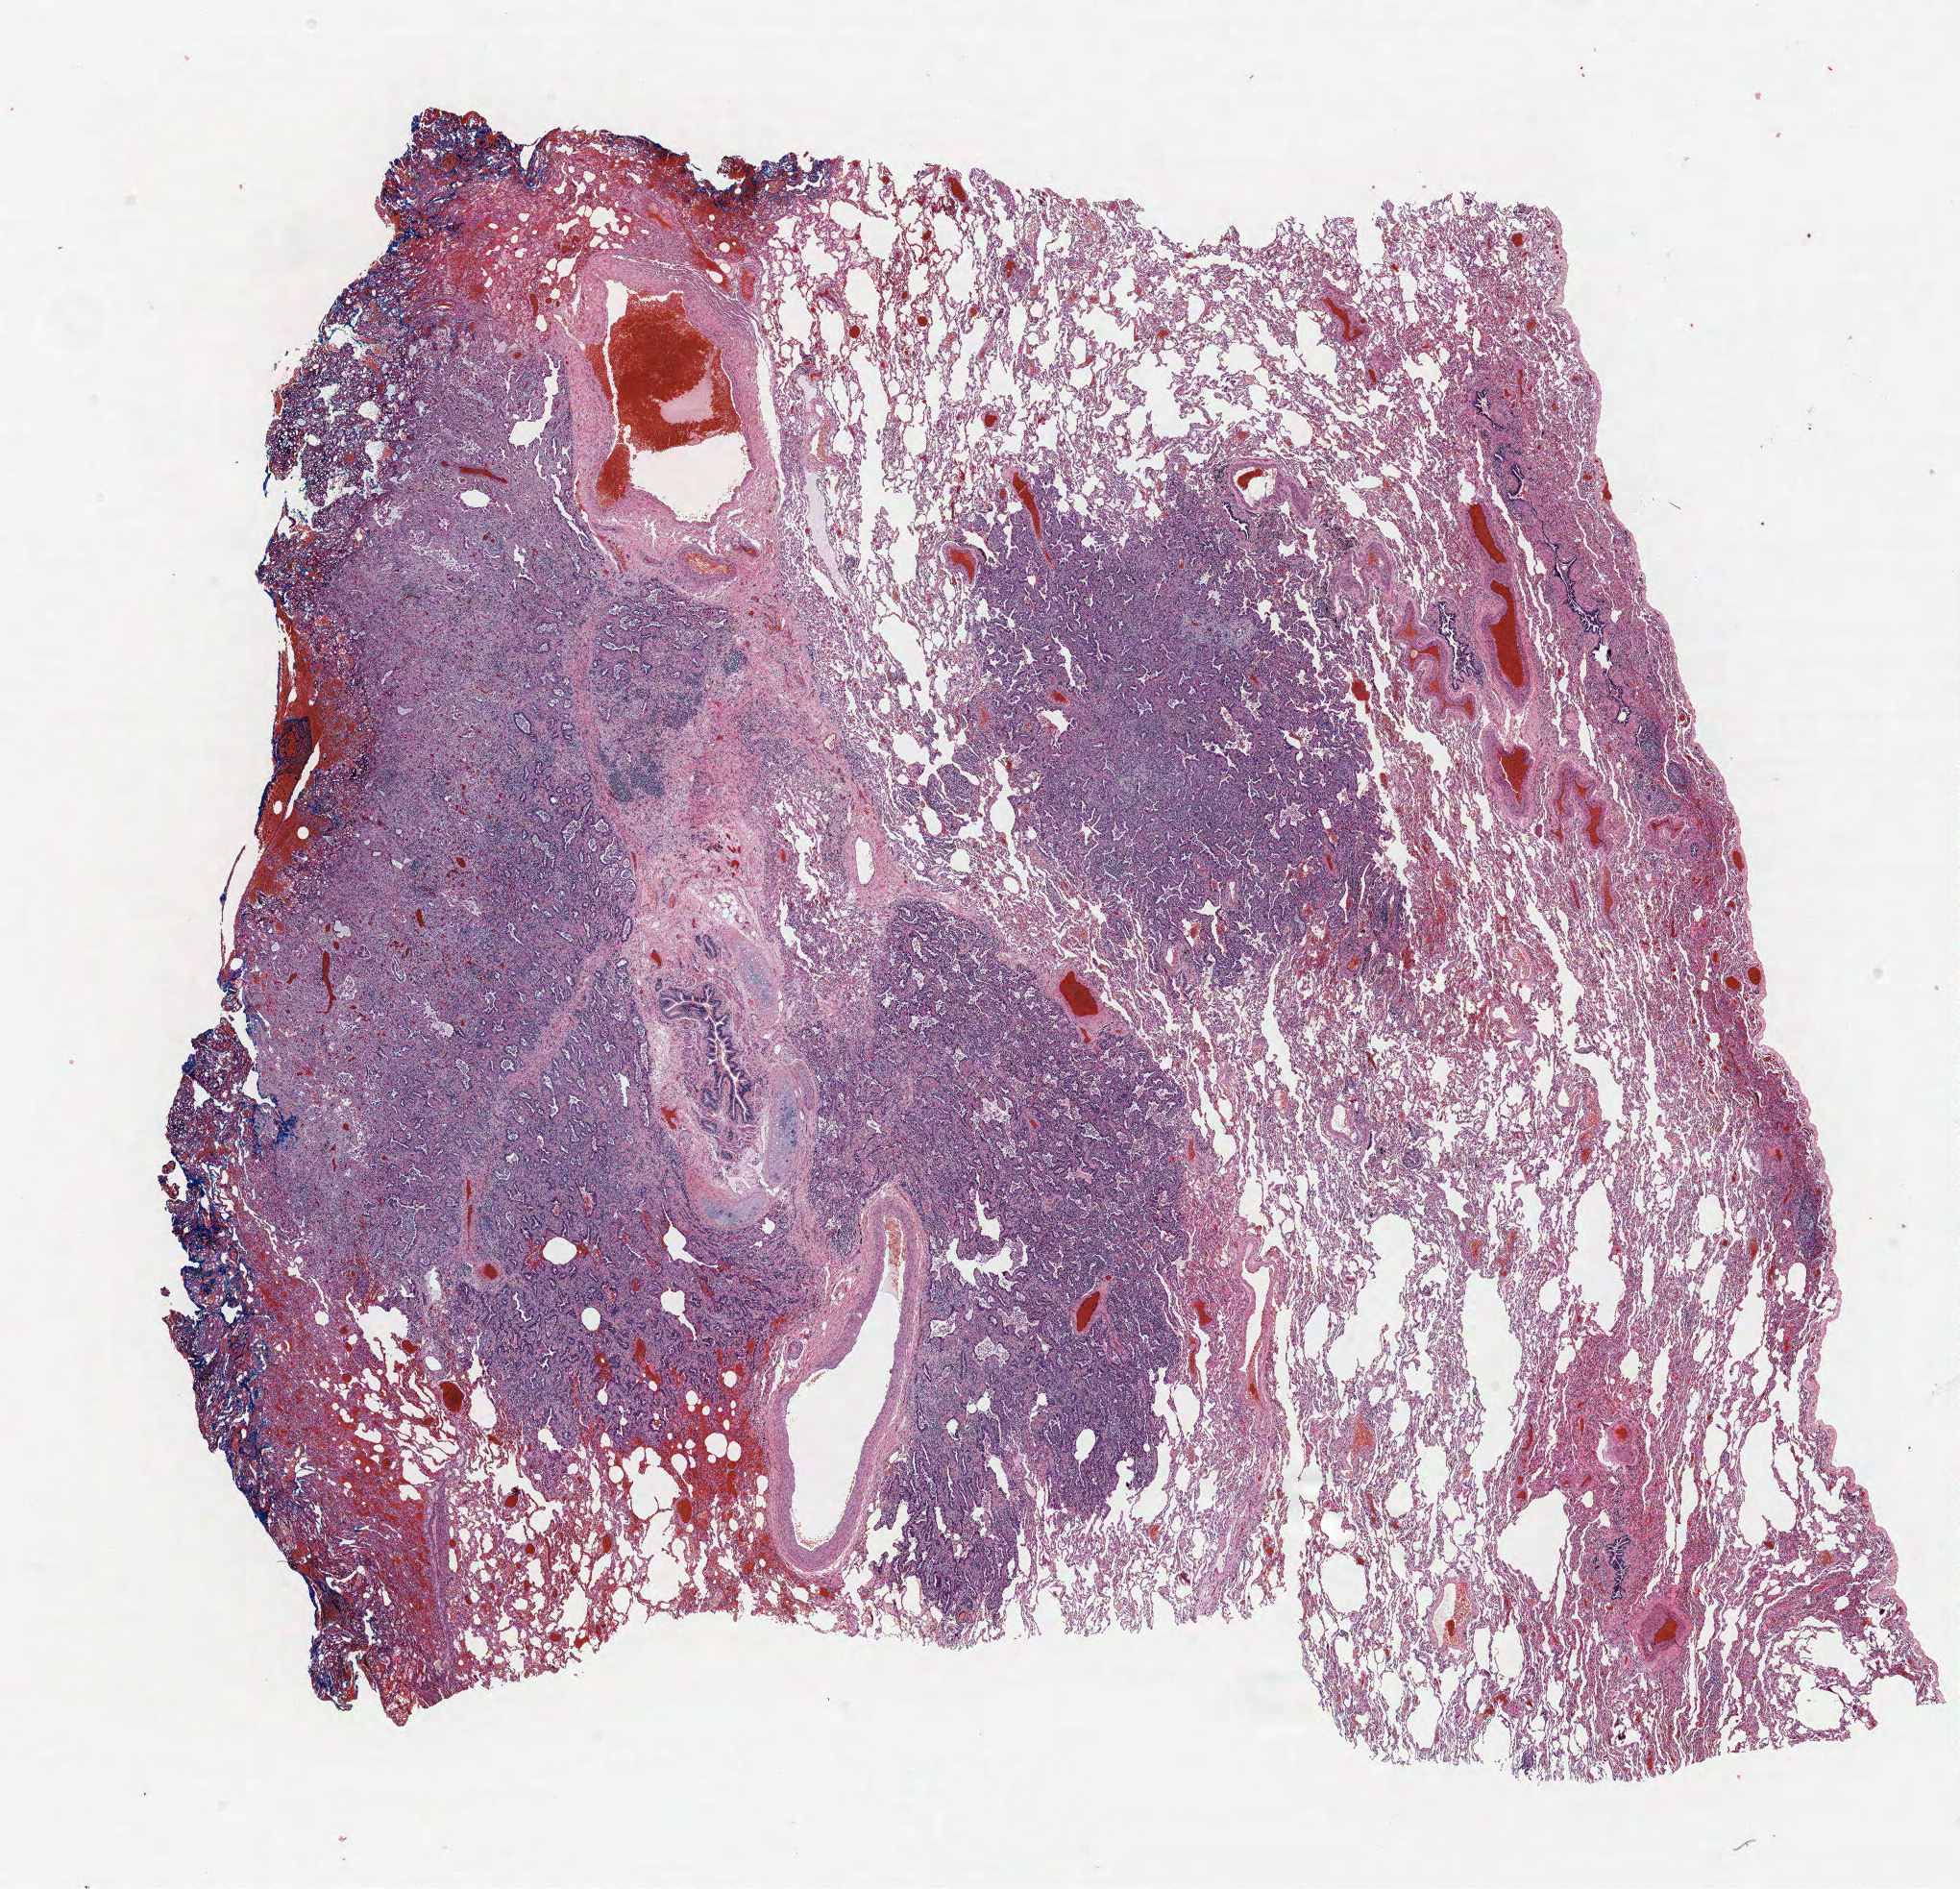
Whole-slide histology image, Hematoxylin and eosin (H&E) stained, shown as a low-resolution overview of the whole scanned area (about 16.3 x 15.7 mm, acquisition: 40x scan), FFPE section, lung tissue. Male, age 56 at enrolment. Former smoker at enrolment. Grade: poorly differentiated (G3).
• primary tumour location (clinical record): right upper lobe
• tumour size (pathology): 12 mm
• participant's lung-cancer diagnosis: Adenocarcinoma, NOS
• stage (AJCC 6th edition): IA